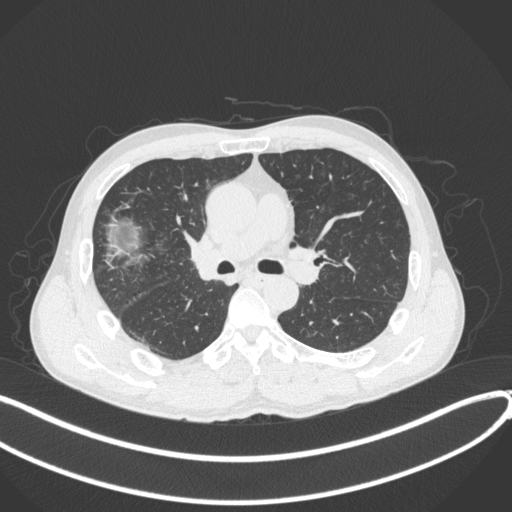
Chest CT, one axial slice; reconstruction kernel B31f; lung window (W 1500 / L -600 HU); 1 mm slice thickness; 512 × 512 image matrix, field of view 400 × 400 mm. Patient: male, 53 years. From the clinical record (not read from this slice): clinical TNM (as recorded): T1b N0 M0.
Structures marked on this image (bounding box drawn by a radiologist):
- lung tumour (recorded histology: squamous cell carcinoma): box from (x=183, y=221) to (x=222, y=286) px